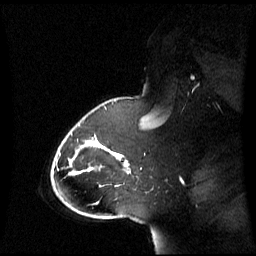
Breast MRI (dynamic contrast-enhanced), one sagittal slice; dynamic contrast-enhanced series, image 2 of 3 at this slice position (ordered by acquisition); 1.5 T; TE 4.2 ms, TR 8.4 ms; 256 × 256 image matrix, field of view 270 × 270 mm. Patient: female, 43 years. From the clinical record (not read from this slice): setting: breast cancer imaged before/during neoadjuvant chemotherapy; receptor status: triple-negative.
Outlined on this slice (semi-automatic segmentation, software-assisted and operator-edited):
- analysis volume of interest (the breast-tissue region the enhancement analysis was run in; not a lesion): bounding box <65,118,143,198> (left, top, right, bottom; pixels)
- tumour enhancement mask (voxels above the 70 % enhancement threshold inside the analysis volume of interest): <94,139,129,167>